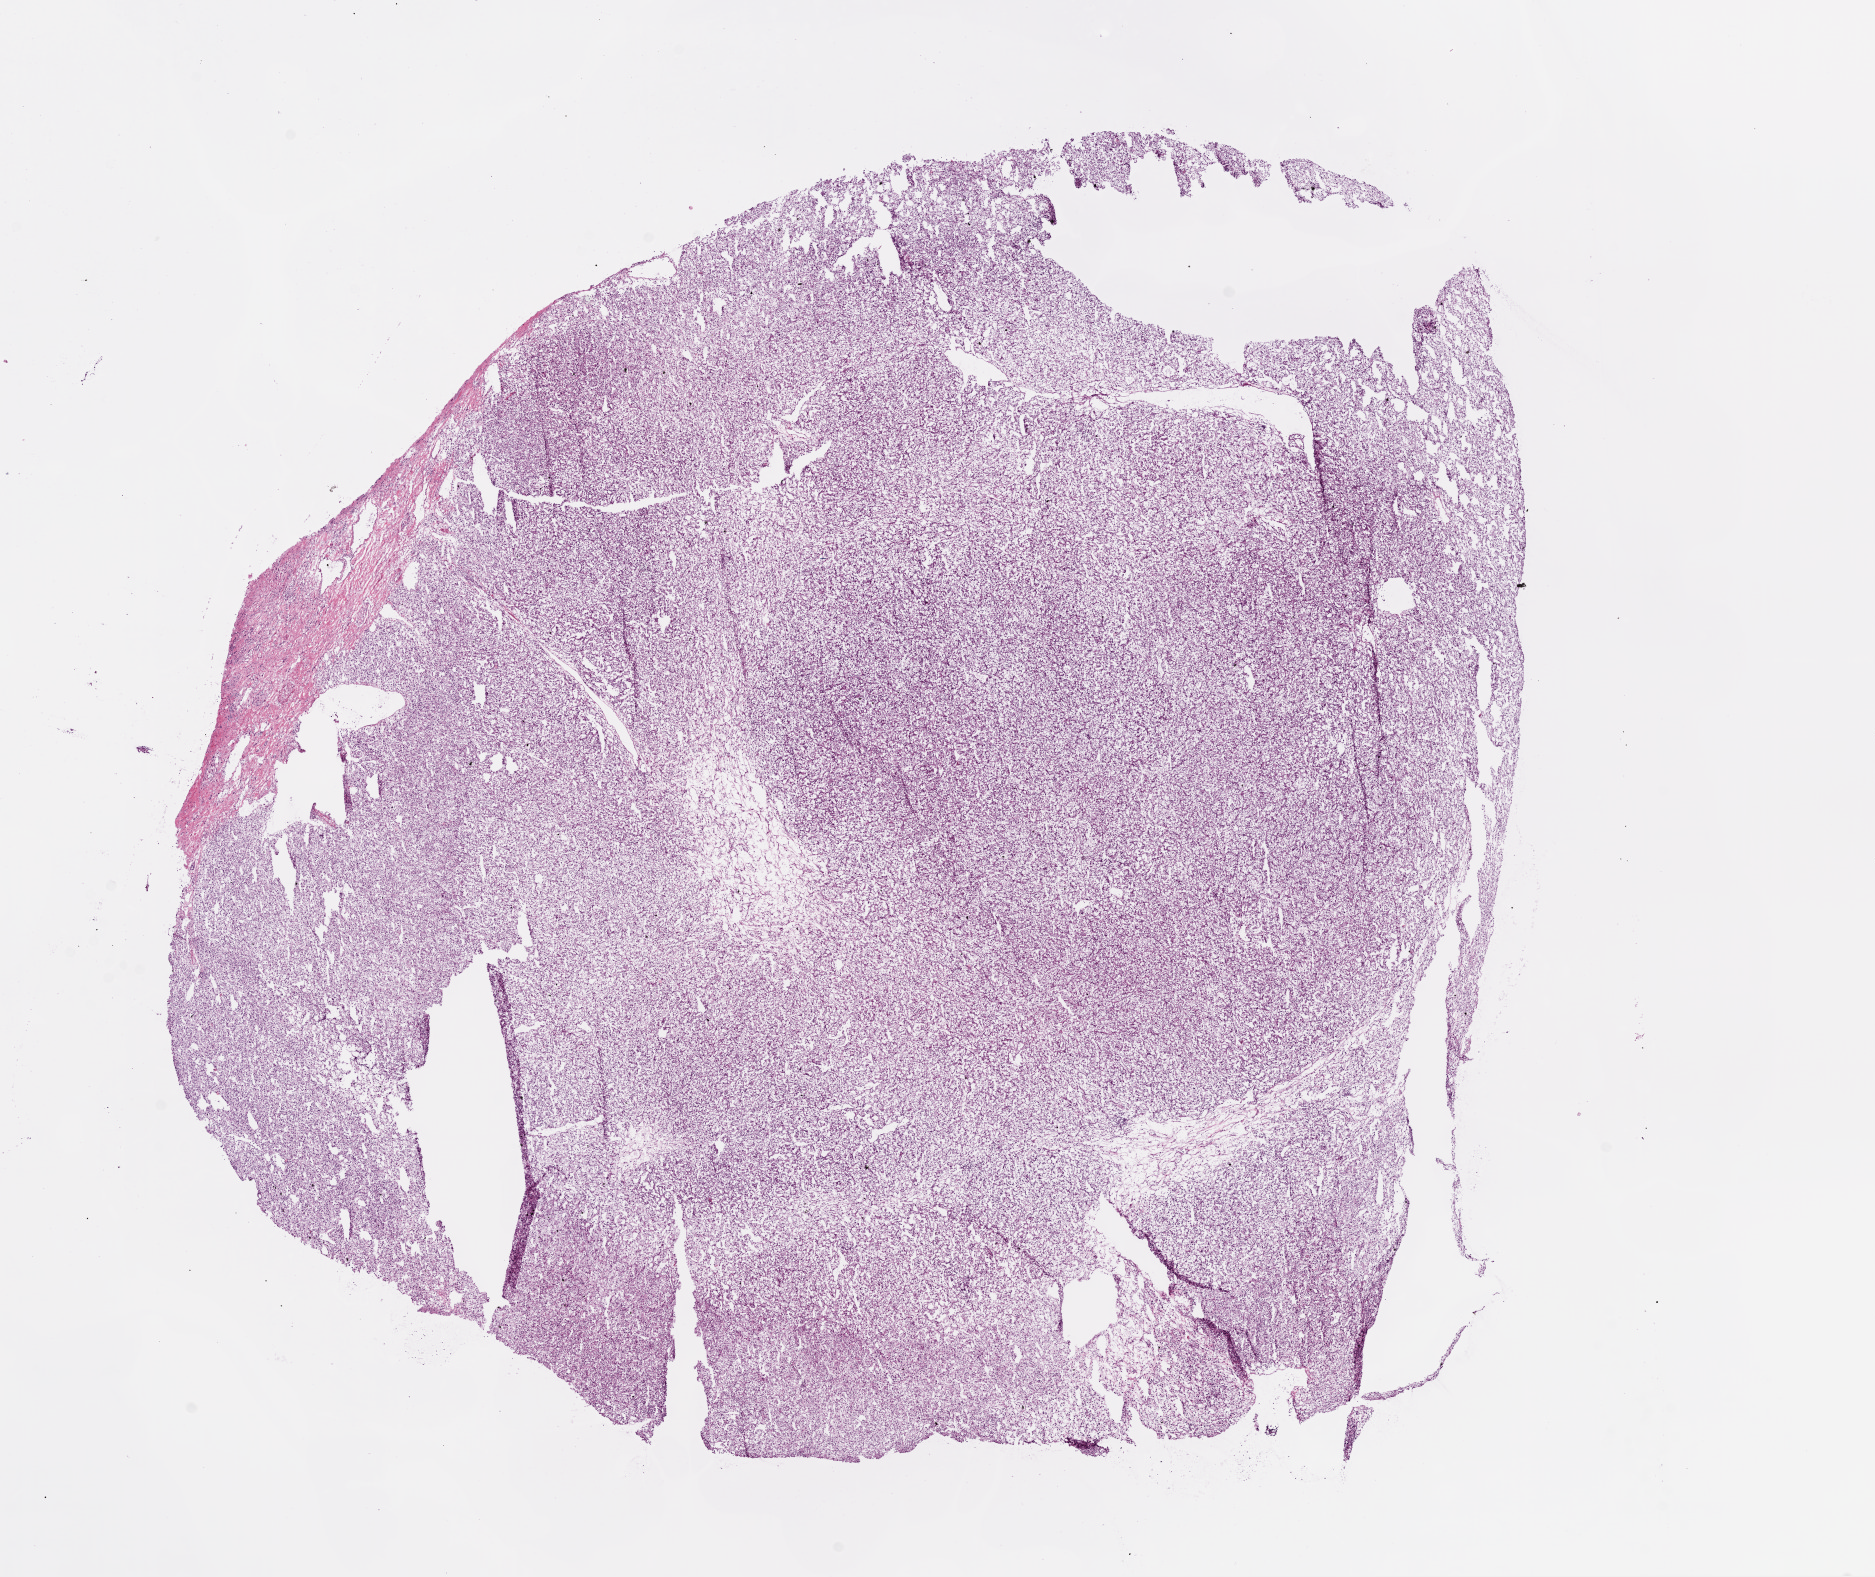
Whole-slide histology image, Hematoxylin and eosin (H&E) stained — a low-resolution overview of the entire scanned area, about 15.0 x 12.7 mm; frozen section; sample: primary tumour, kidney. Male, age 53 years at initial diagnosis. Histologic grade: G2 (moderately differentiated). Composition of this section per pathologist review: tumour cells 92%, tumour nuclei 85%, normal cells 0%, stromal cells 8%, necrosis 0%.
Pathologic diagnosis: Clear cell adenocarcinoma, NOS. Laterality: left. AJCC pathologic stage: I (6th edition).